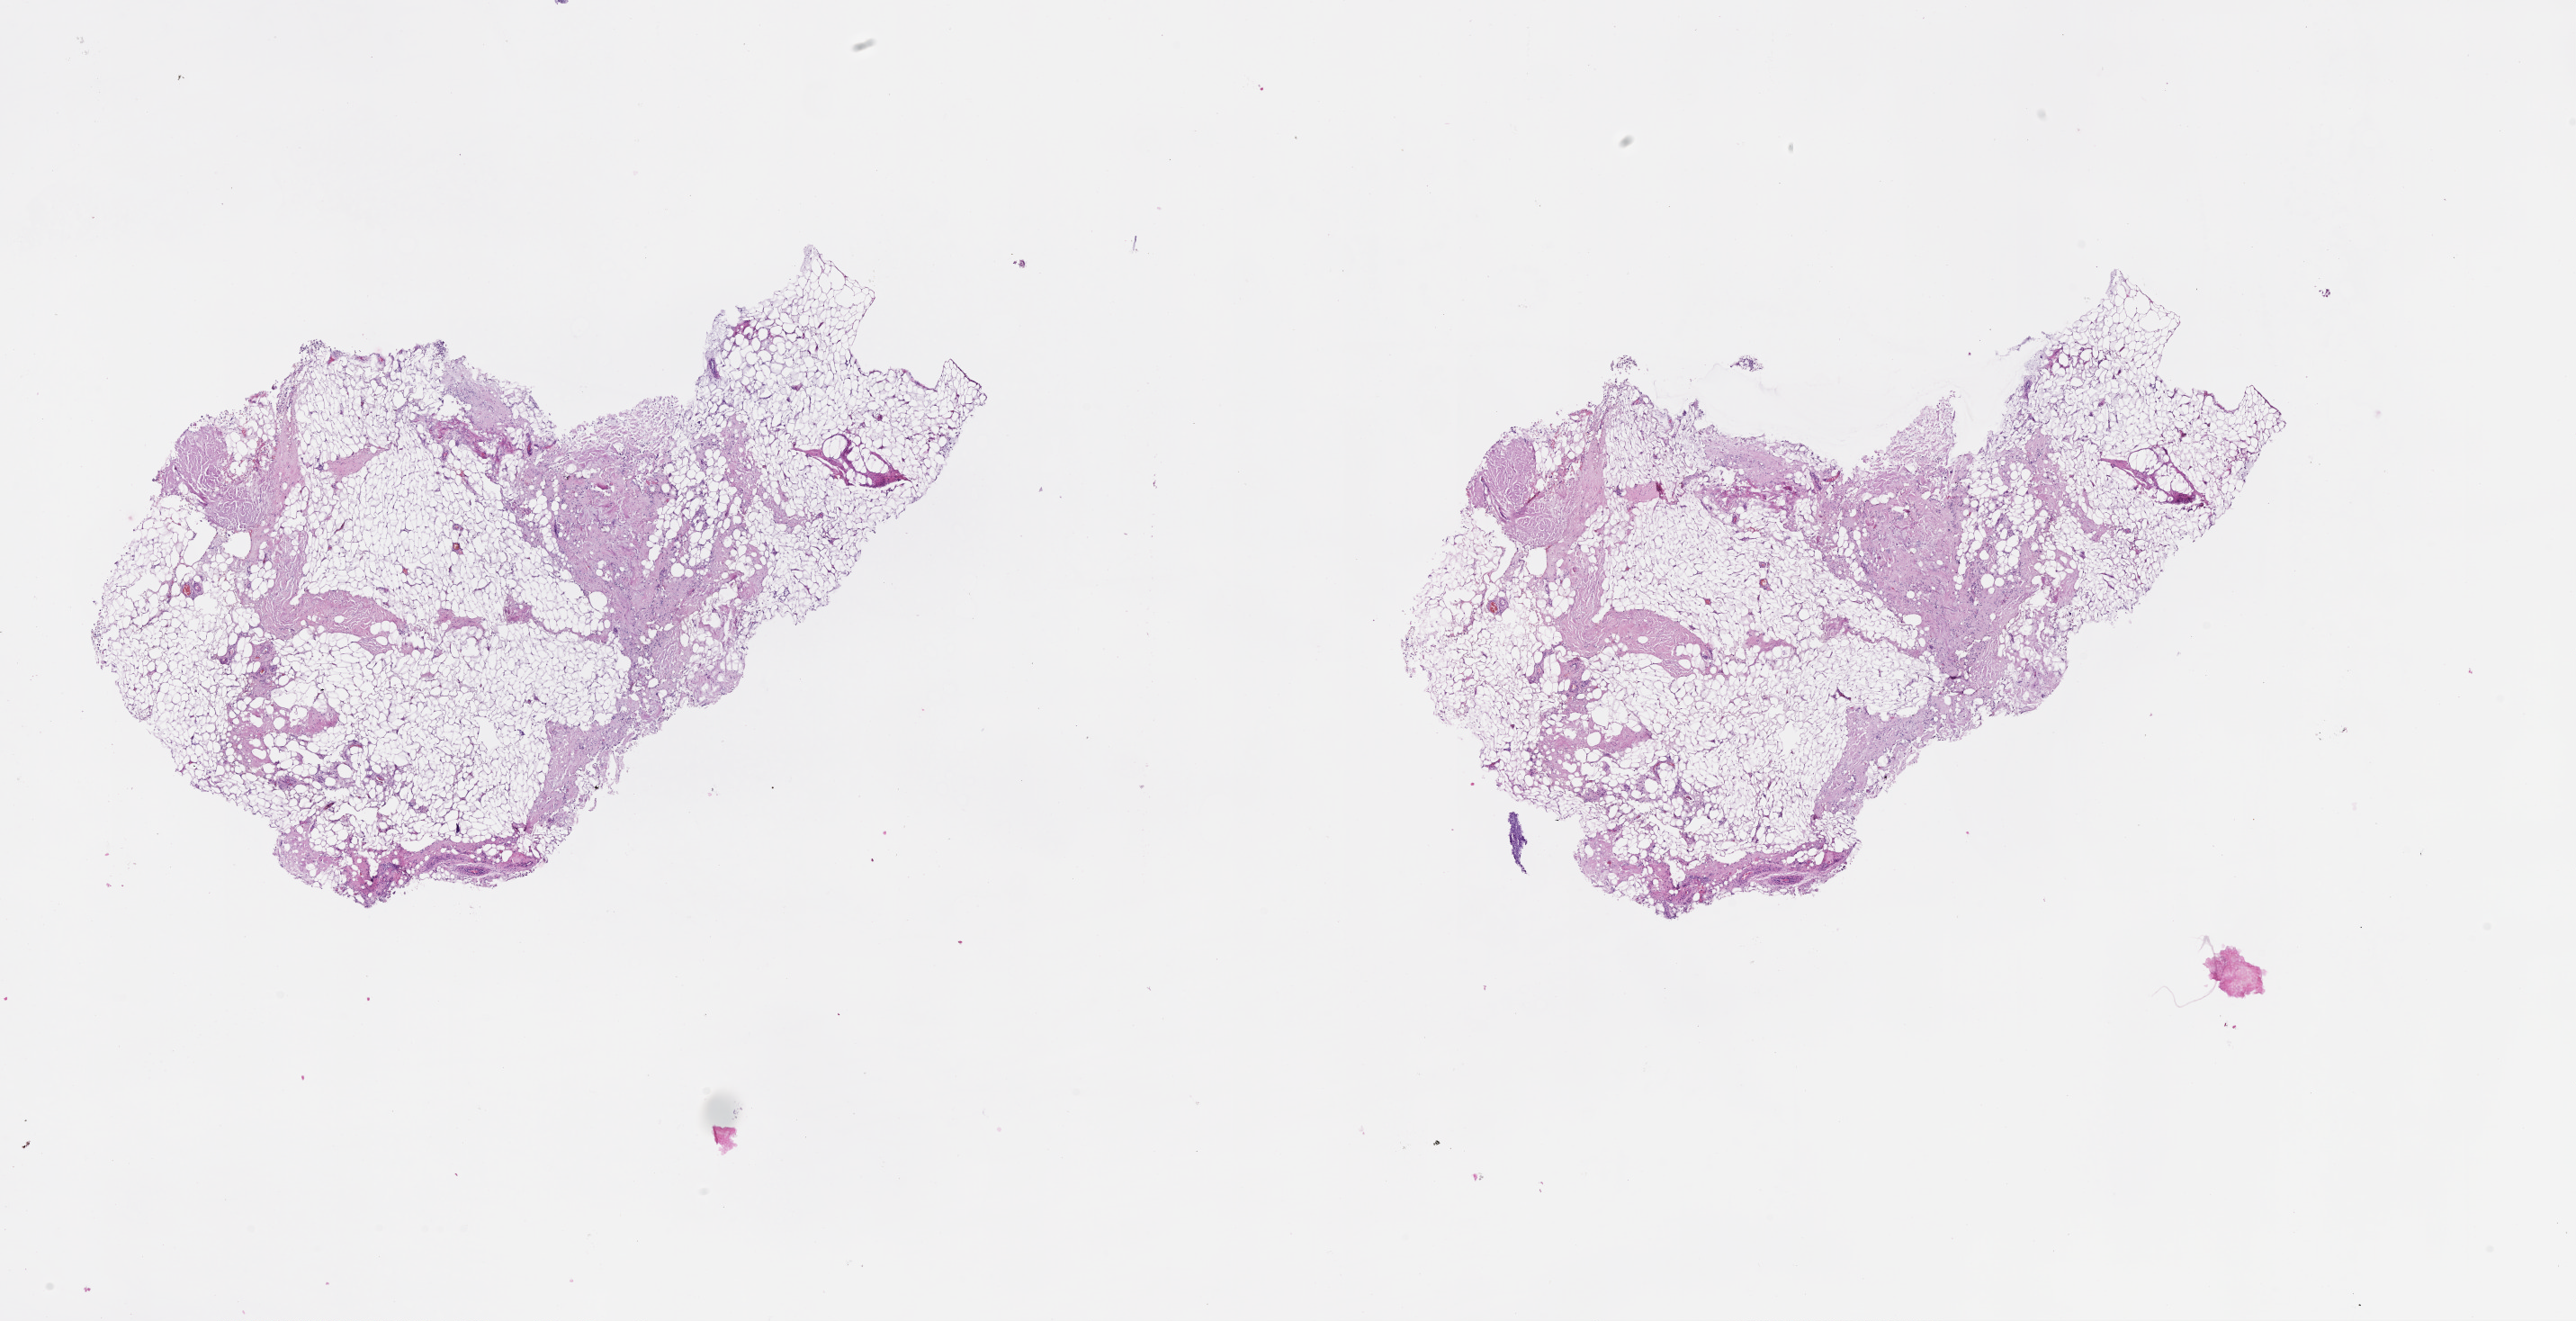
Whole-slide histology image, H&E-stained, low-resolution overview of the scanned area, about 23.1 x 11.8 mm (acquisition: 20x scan). Male, 72 y/o.
* patient diagnosis: Malignant melanoma, NOS